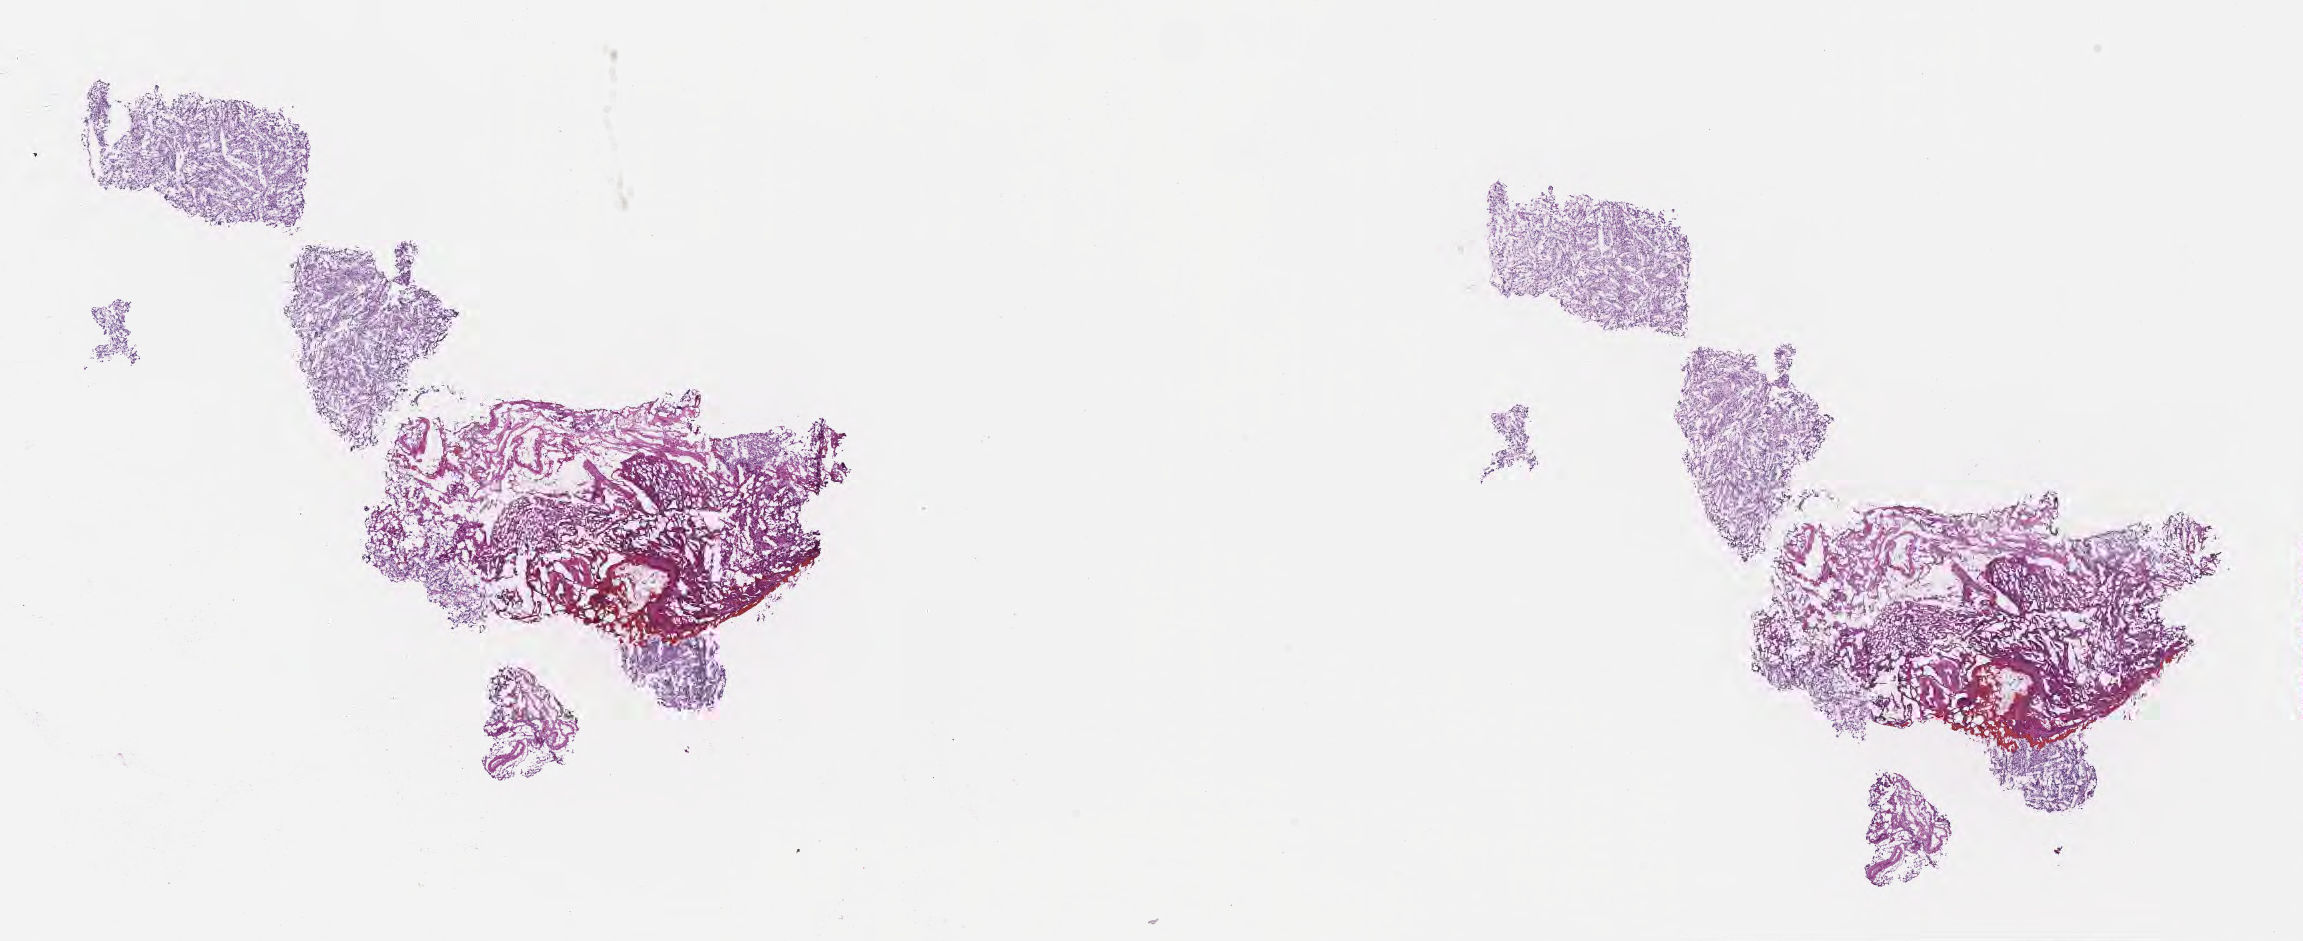
H&E whole-slide image — a low-resolution overview of the entire scanned area, about 18.6 x 7.6 mm. Cryosection. Specimen: primary tumor. Anatomic site: brain. Patient: male, age at initial diagnosis 66 years.
Histologic diagnosis: Gliosarcoma.